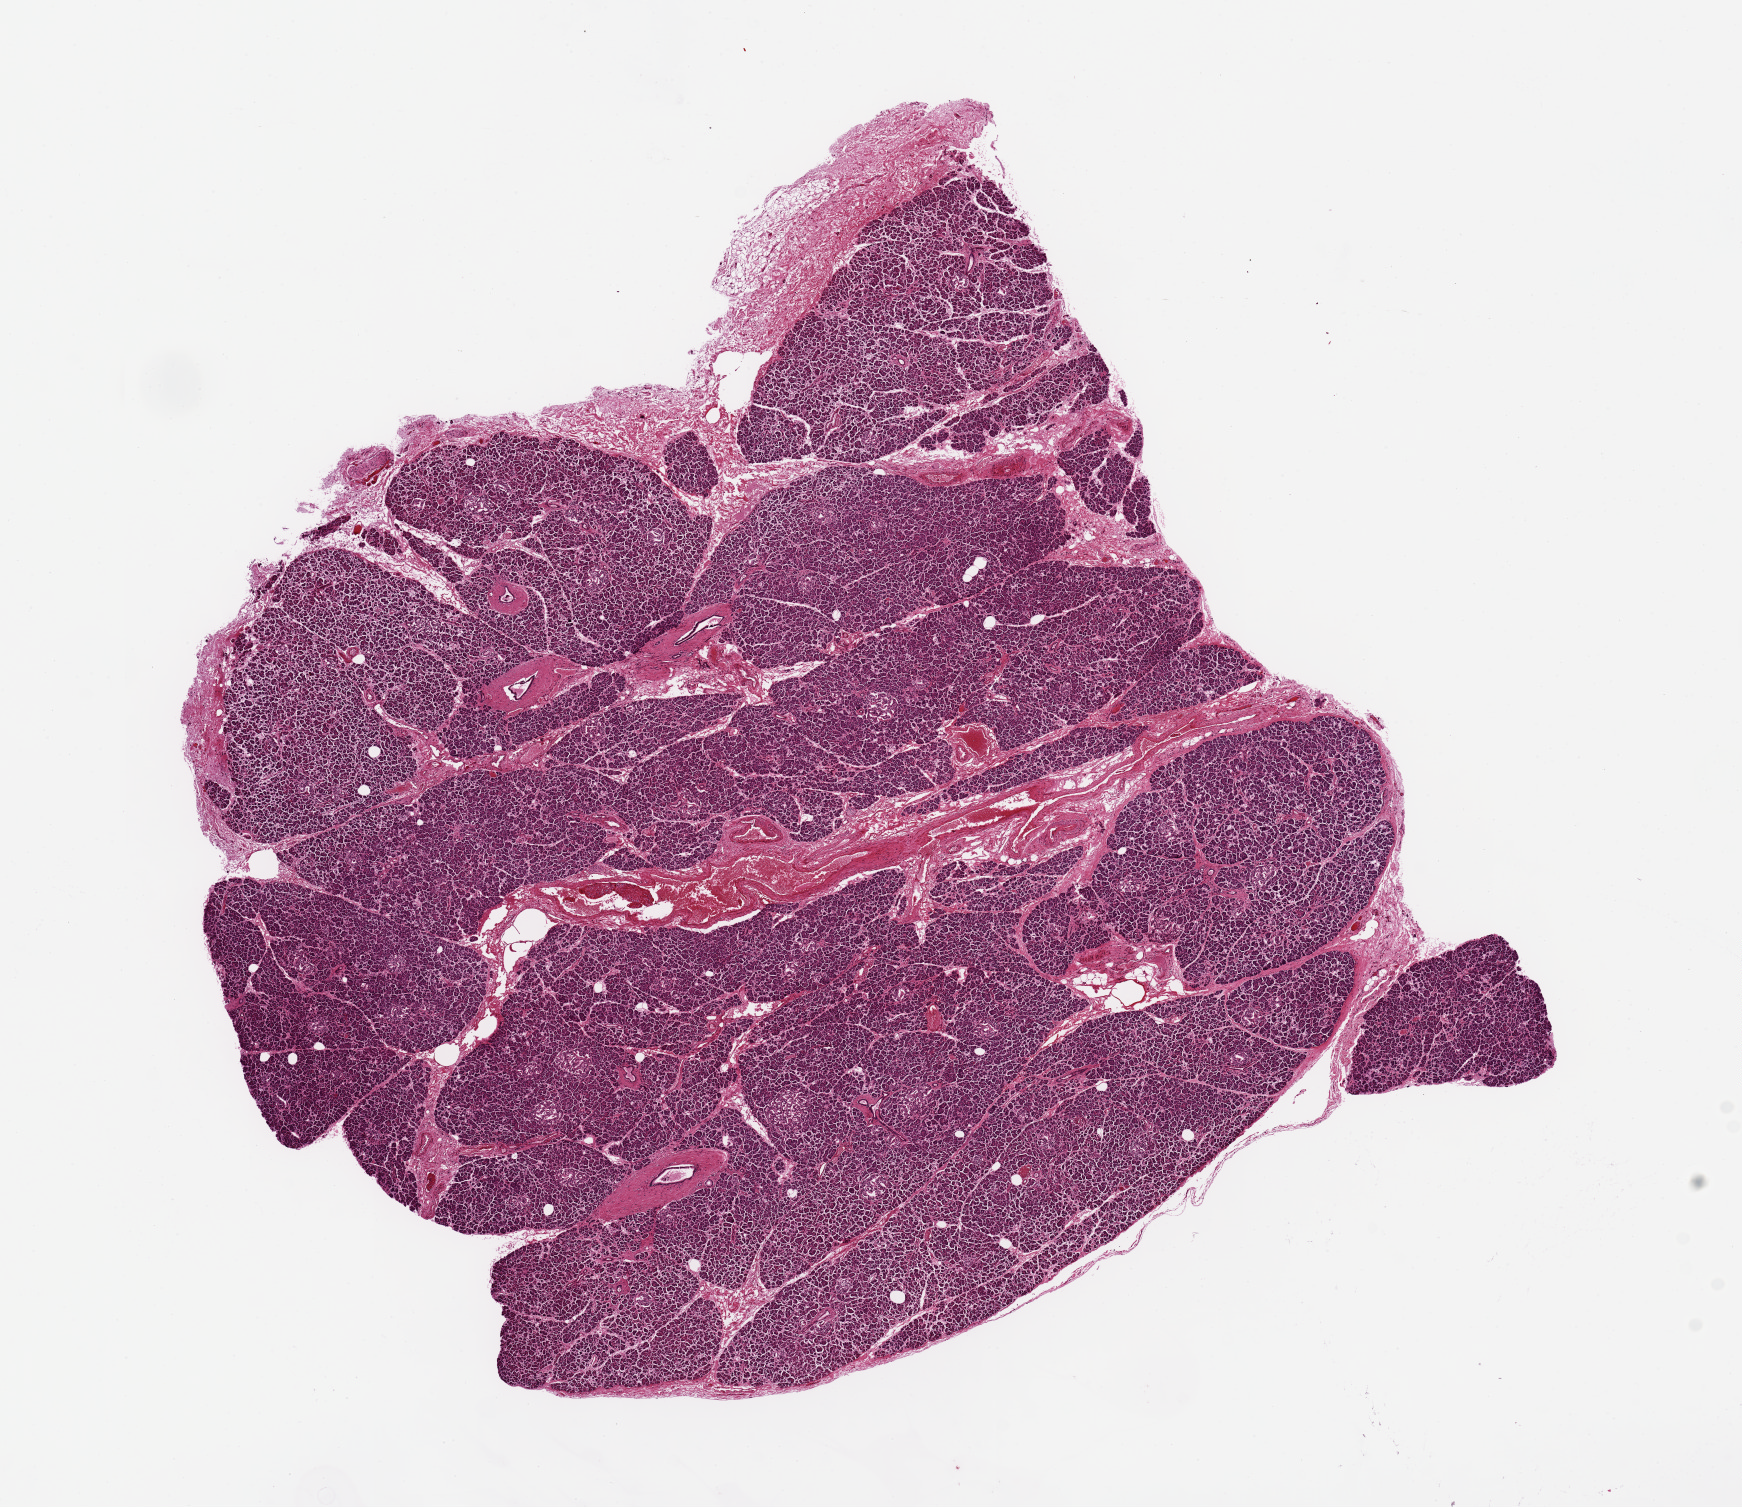
Digitized H&E-stained section, a low-resolution overview of the entire scanned area, about 13.8 x 11.9 mm (acquisition: 20x scan). PAXgene-fixed paraffin-embedded (PFPE) section. Section of pancreas (target tissue). Tissue donor sample. Donor: female.
Reviewer comment on this tissue sample: 10x9.5 mm.